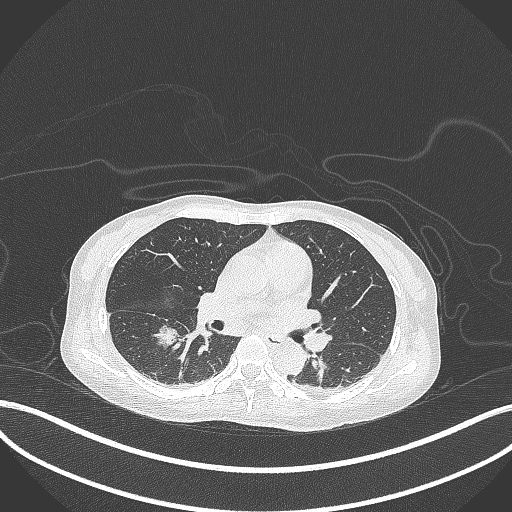
Chest CT, one axial slice; position 166 of 261 along the scan axis; 120 kVp; lung window (W 1500 / L -600 HU); 1 mm slice thickness; 512 × 512 image matrix, field of view 400 × 400 mm. Female patient, age 44 years. From the clinical record (not read from this slice): clinical TNM (as recorded): T1c N0 M0.
Outlined on this slice (bounding box drawn by a radiologist):
- lung tumour (recorded histology: adenocarcinoma): bounding box <151,323,181,350> (left, top, right, bottom; pixels)